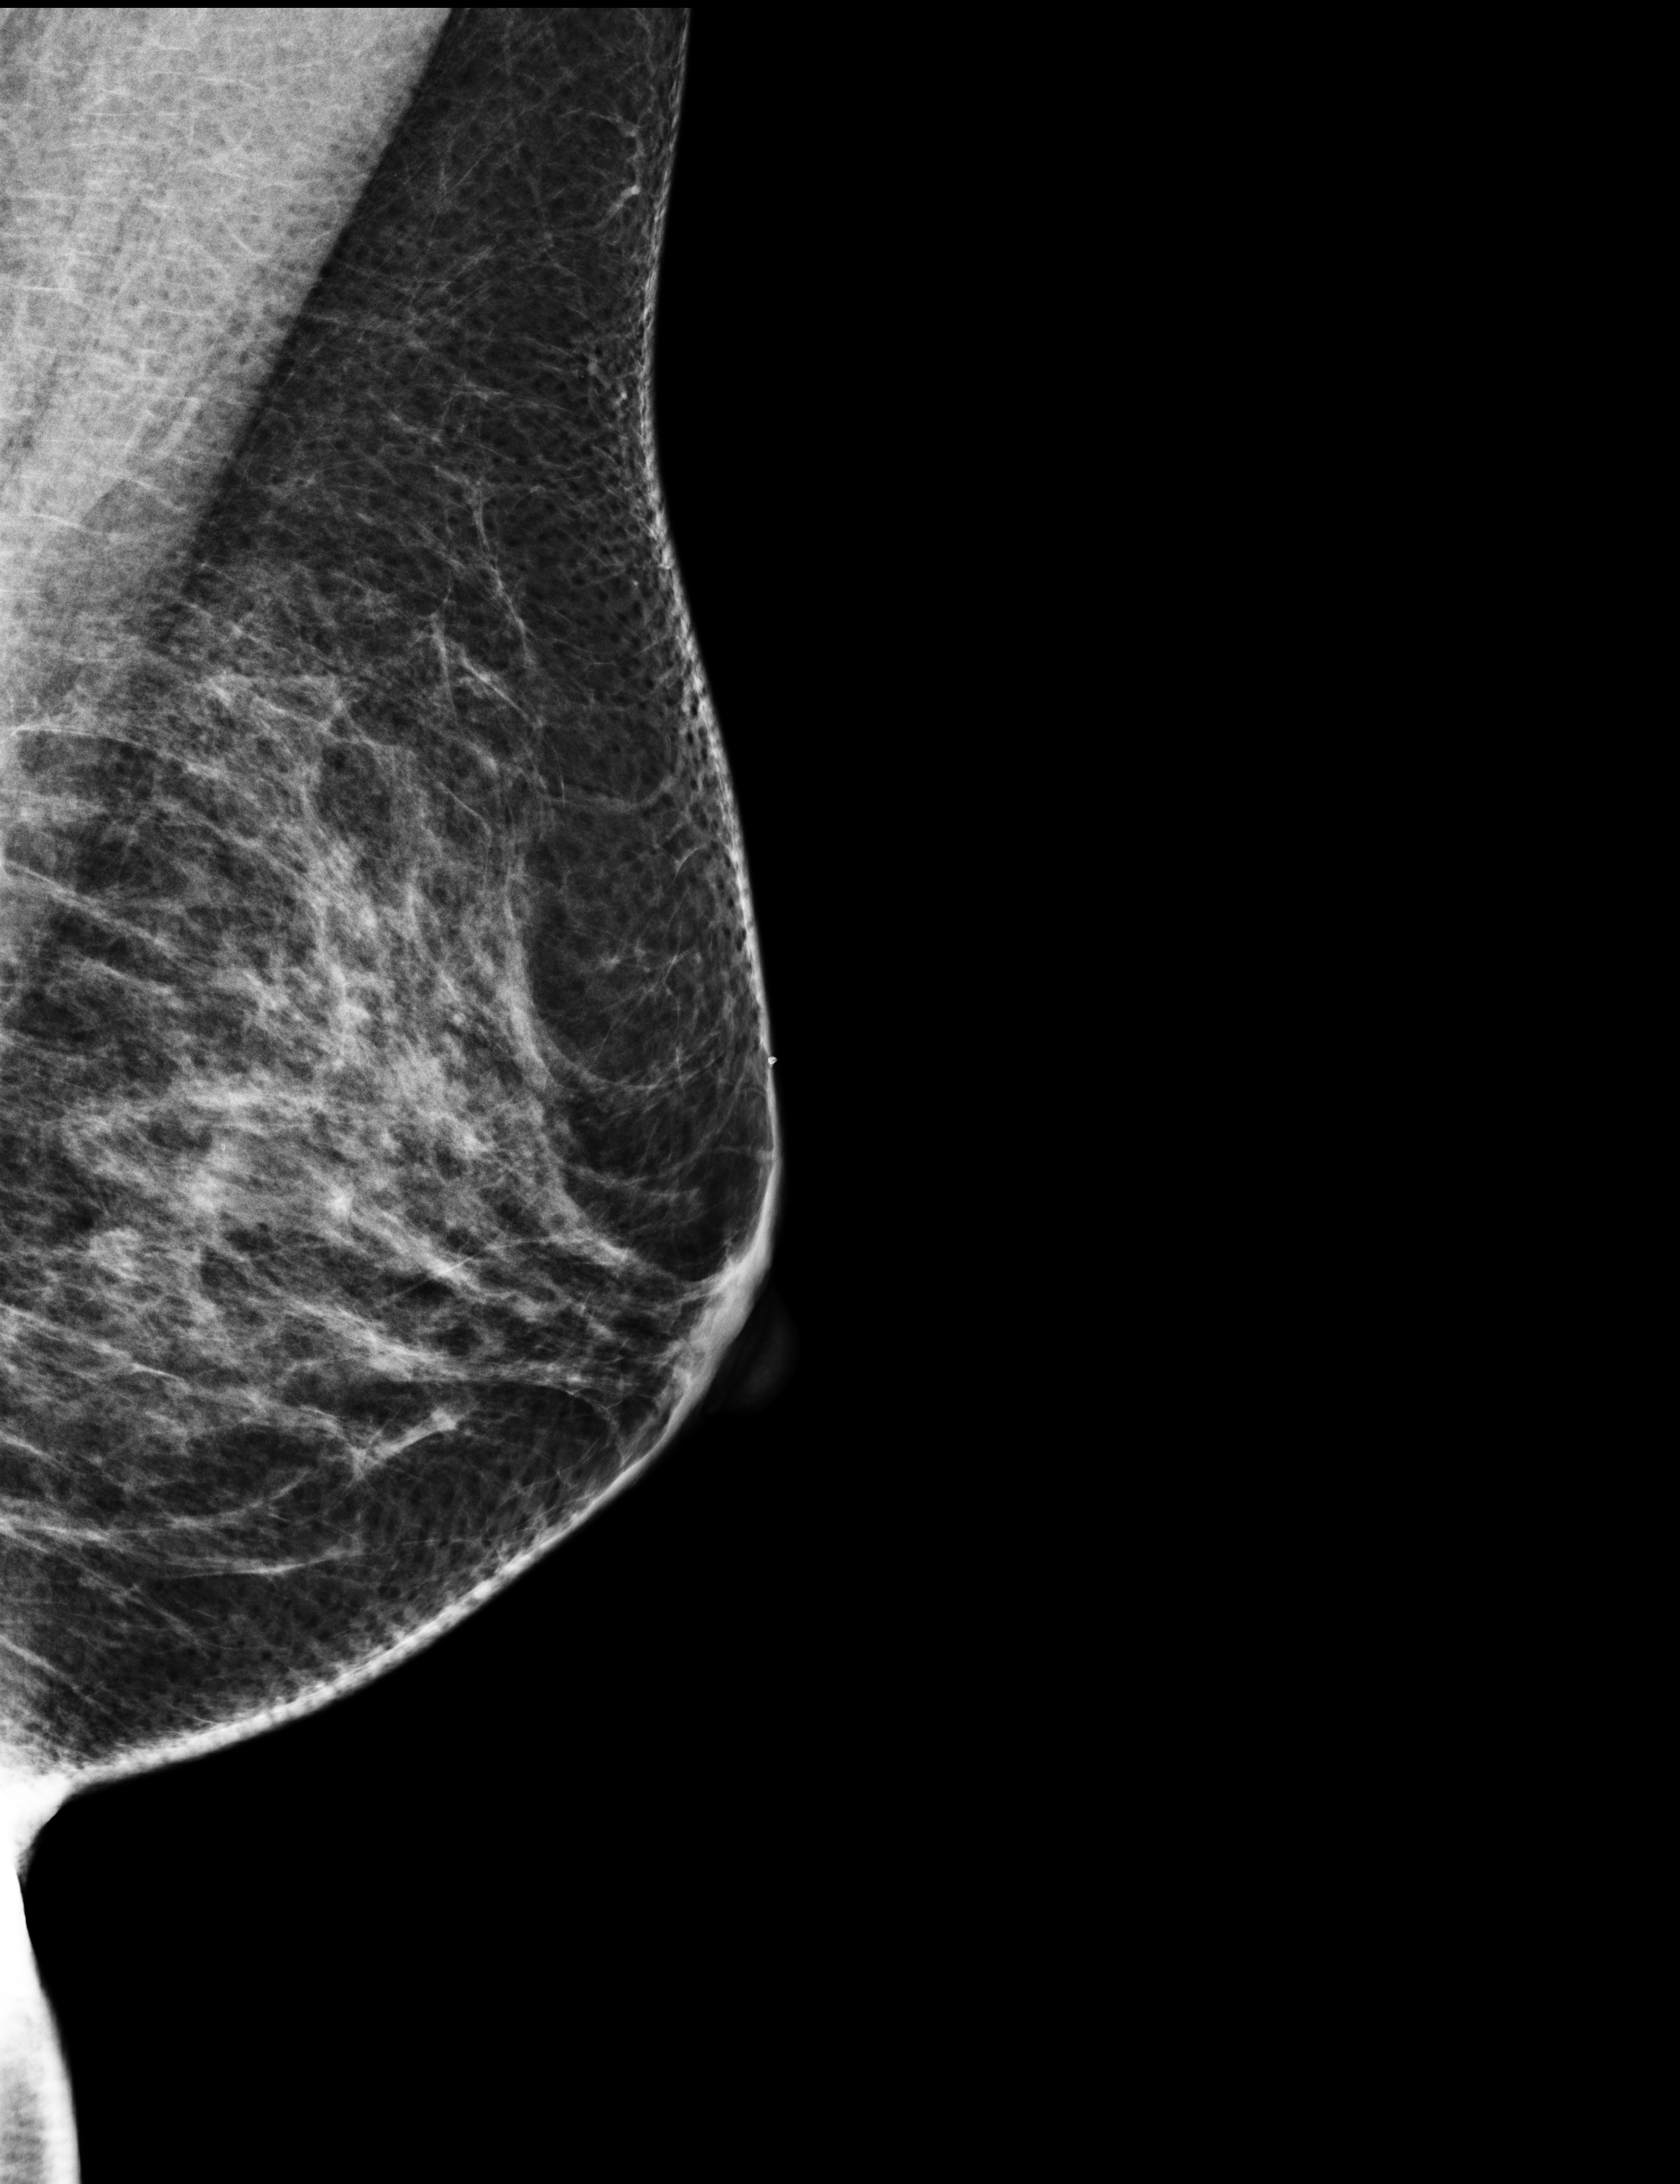
Full-field digital mammogram (FFDM), left breast, mediolateral oblique (MLO) view, annual screening mammography examination, system: Selenia Dimensions. Patient aged 43 years (female).
Breast density at the screening exam (both breasts): heterogeneously dense (BI-RADS density category c). Final BI-RADS assessment for this screening round (tomosynthesis exam, both breasts): category 1. Recall: no recall after this screen.